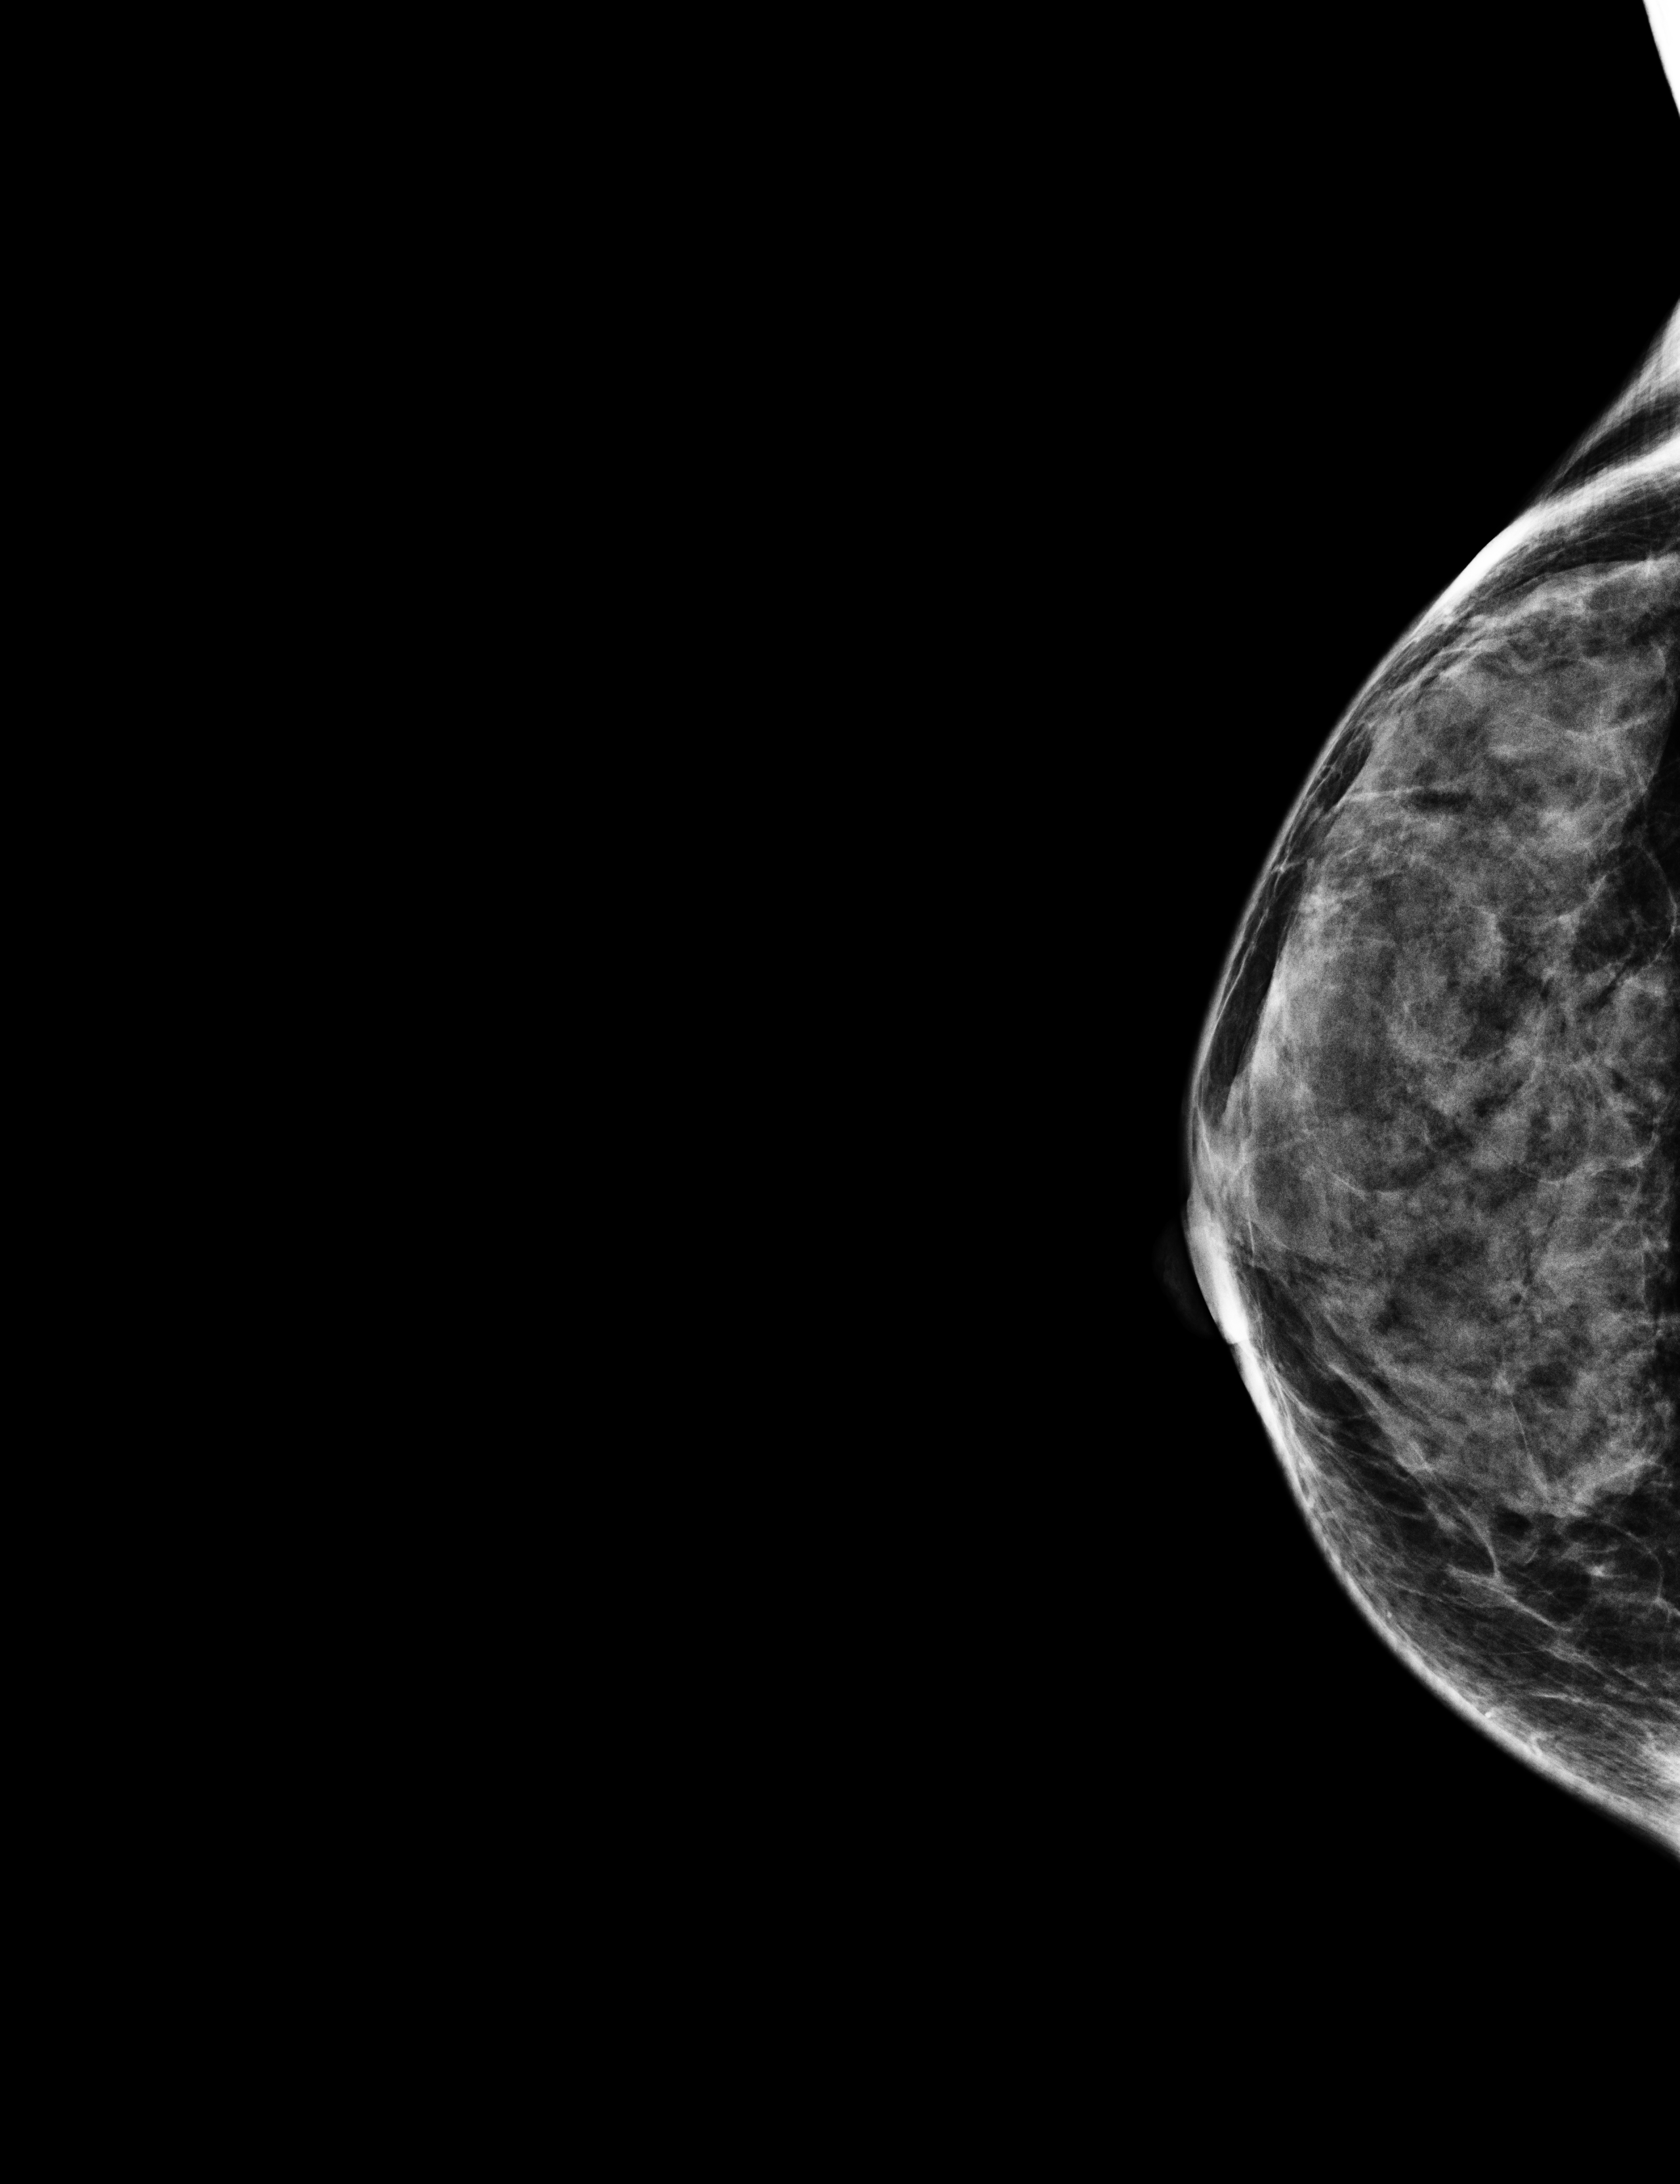
Full-field digital mammogram (FFDM); right breast; cranio-caudal projection; annual screening mammography examination; compressed breast thickness 40 mm. Patient aged 43 years (female).
- BI-RADS breast density category at the screening exam (both breasts, scale 1–4): 3
- final BI-RADS assessment for this screening round (tomosynthesis exam, both breasts): category 2
- recall: no recall after this screen